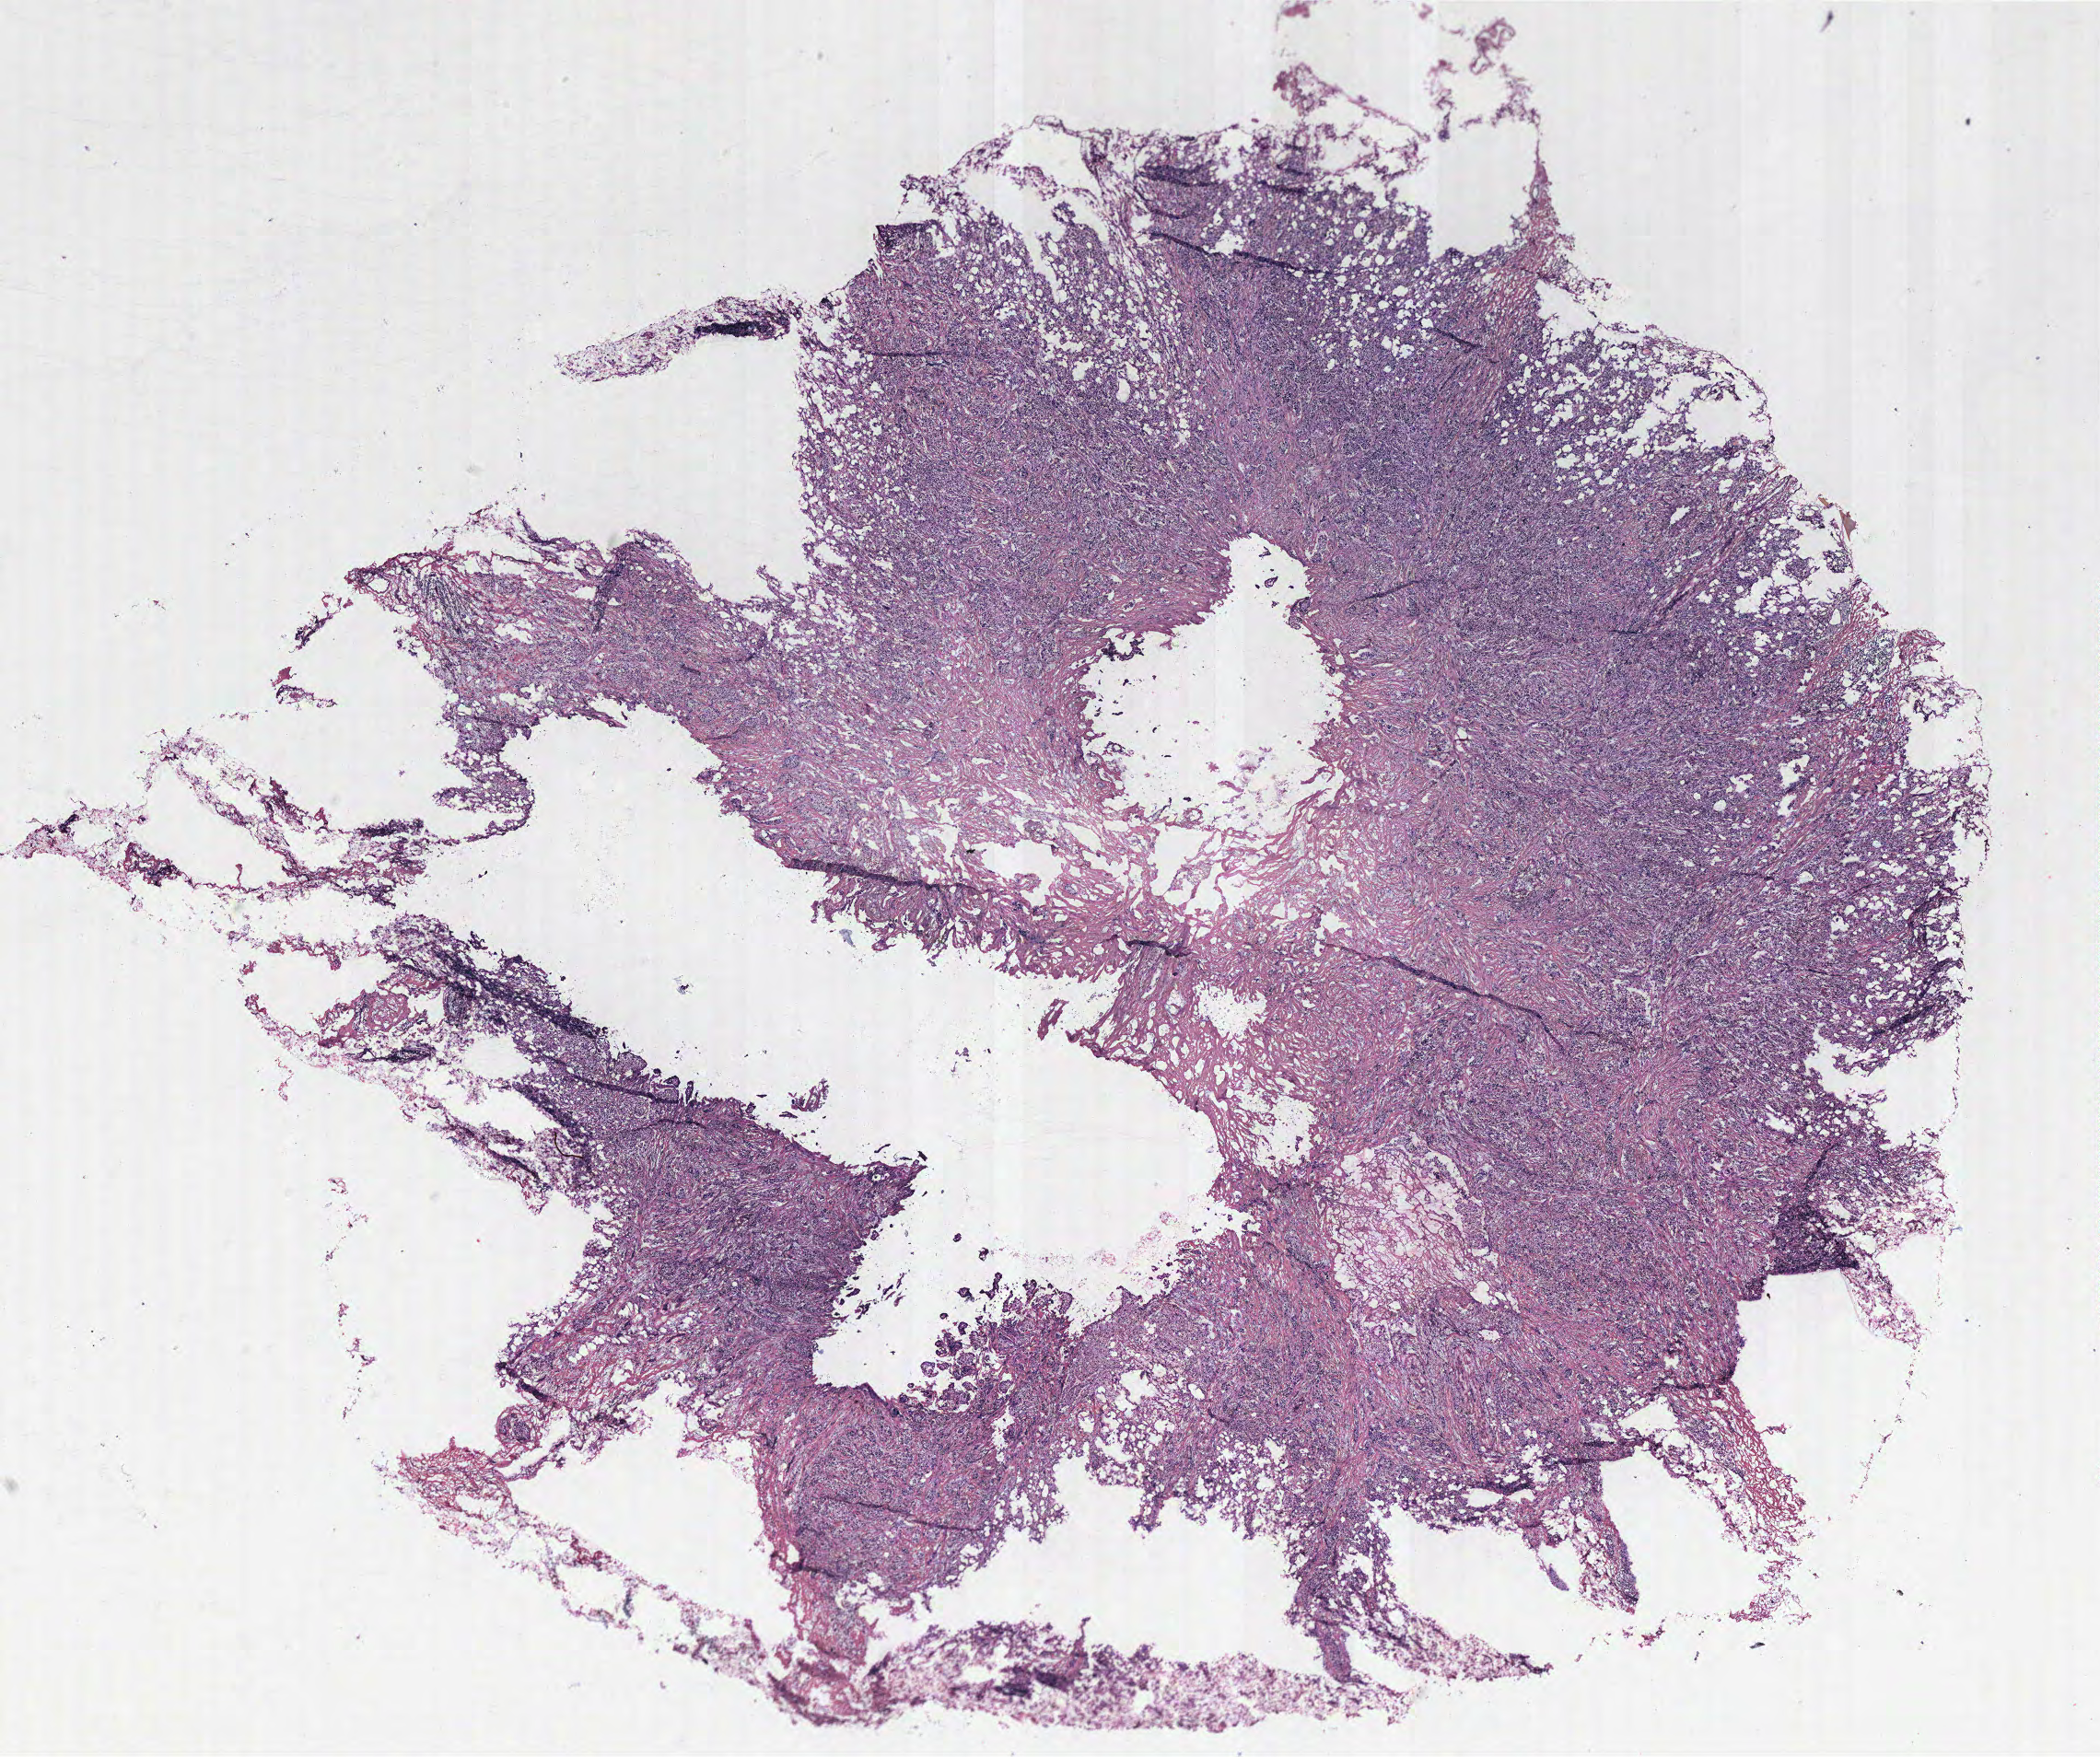
Whole-slide histology image, Hematoxylin and eosin (H&E) stained — low-resolution overview of the scanned area, about 18.2 x 15.3 mm (from a 40x scan), breast, tissue type not recorded. Female, 65 y/o.
Patient diagnosis: Infiltrating duct carcinoma, NOS.